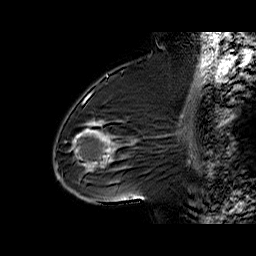
Breast MRI (dynamic contrast-enhanced), one sagittal slice; dynamic contrast-enhanced series, time point 2 of 6 at this slice position (early post-contrast); 1.5 T; TE 6.3 ms, TR 32.4 ms; 4 mm slice thickness; 256 × 256 image matrix, field of view 200 × 200 mm. Female patient. From the clinical record (not read from this slice): setting: breast cancer imaged before/during neoadjuvant chemotherapy; receptor status: triple-negative.
Structures marked on this image (semi-automatically segmented with operator editing):
- analysis volume of interest (the breast-tissue region the enhancement analysis was run in; not a lesion): bounding box <65,88,146,187> (left, top, right, bottom; pixels)
- tumour enhancement mask (voxels above the 100 % enhancement threshold inside the analysis volume of interest): <74,122,114,165>